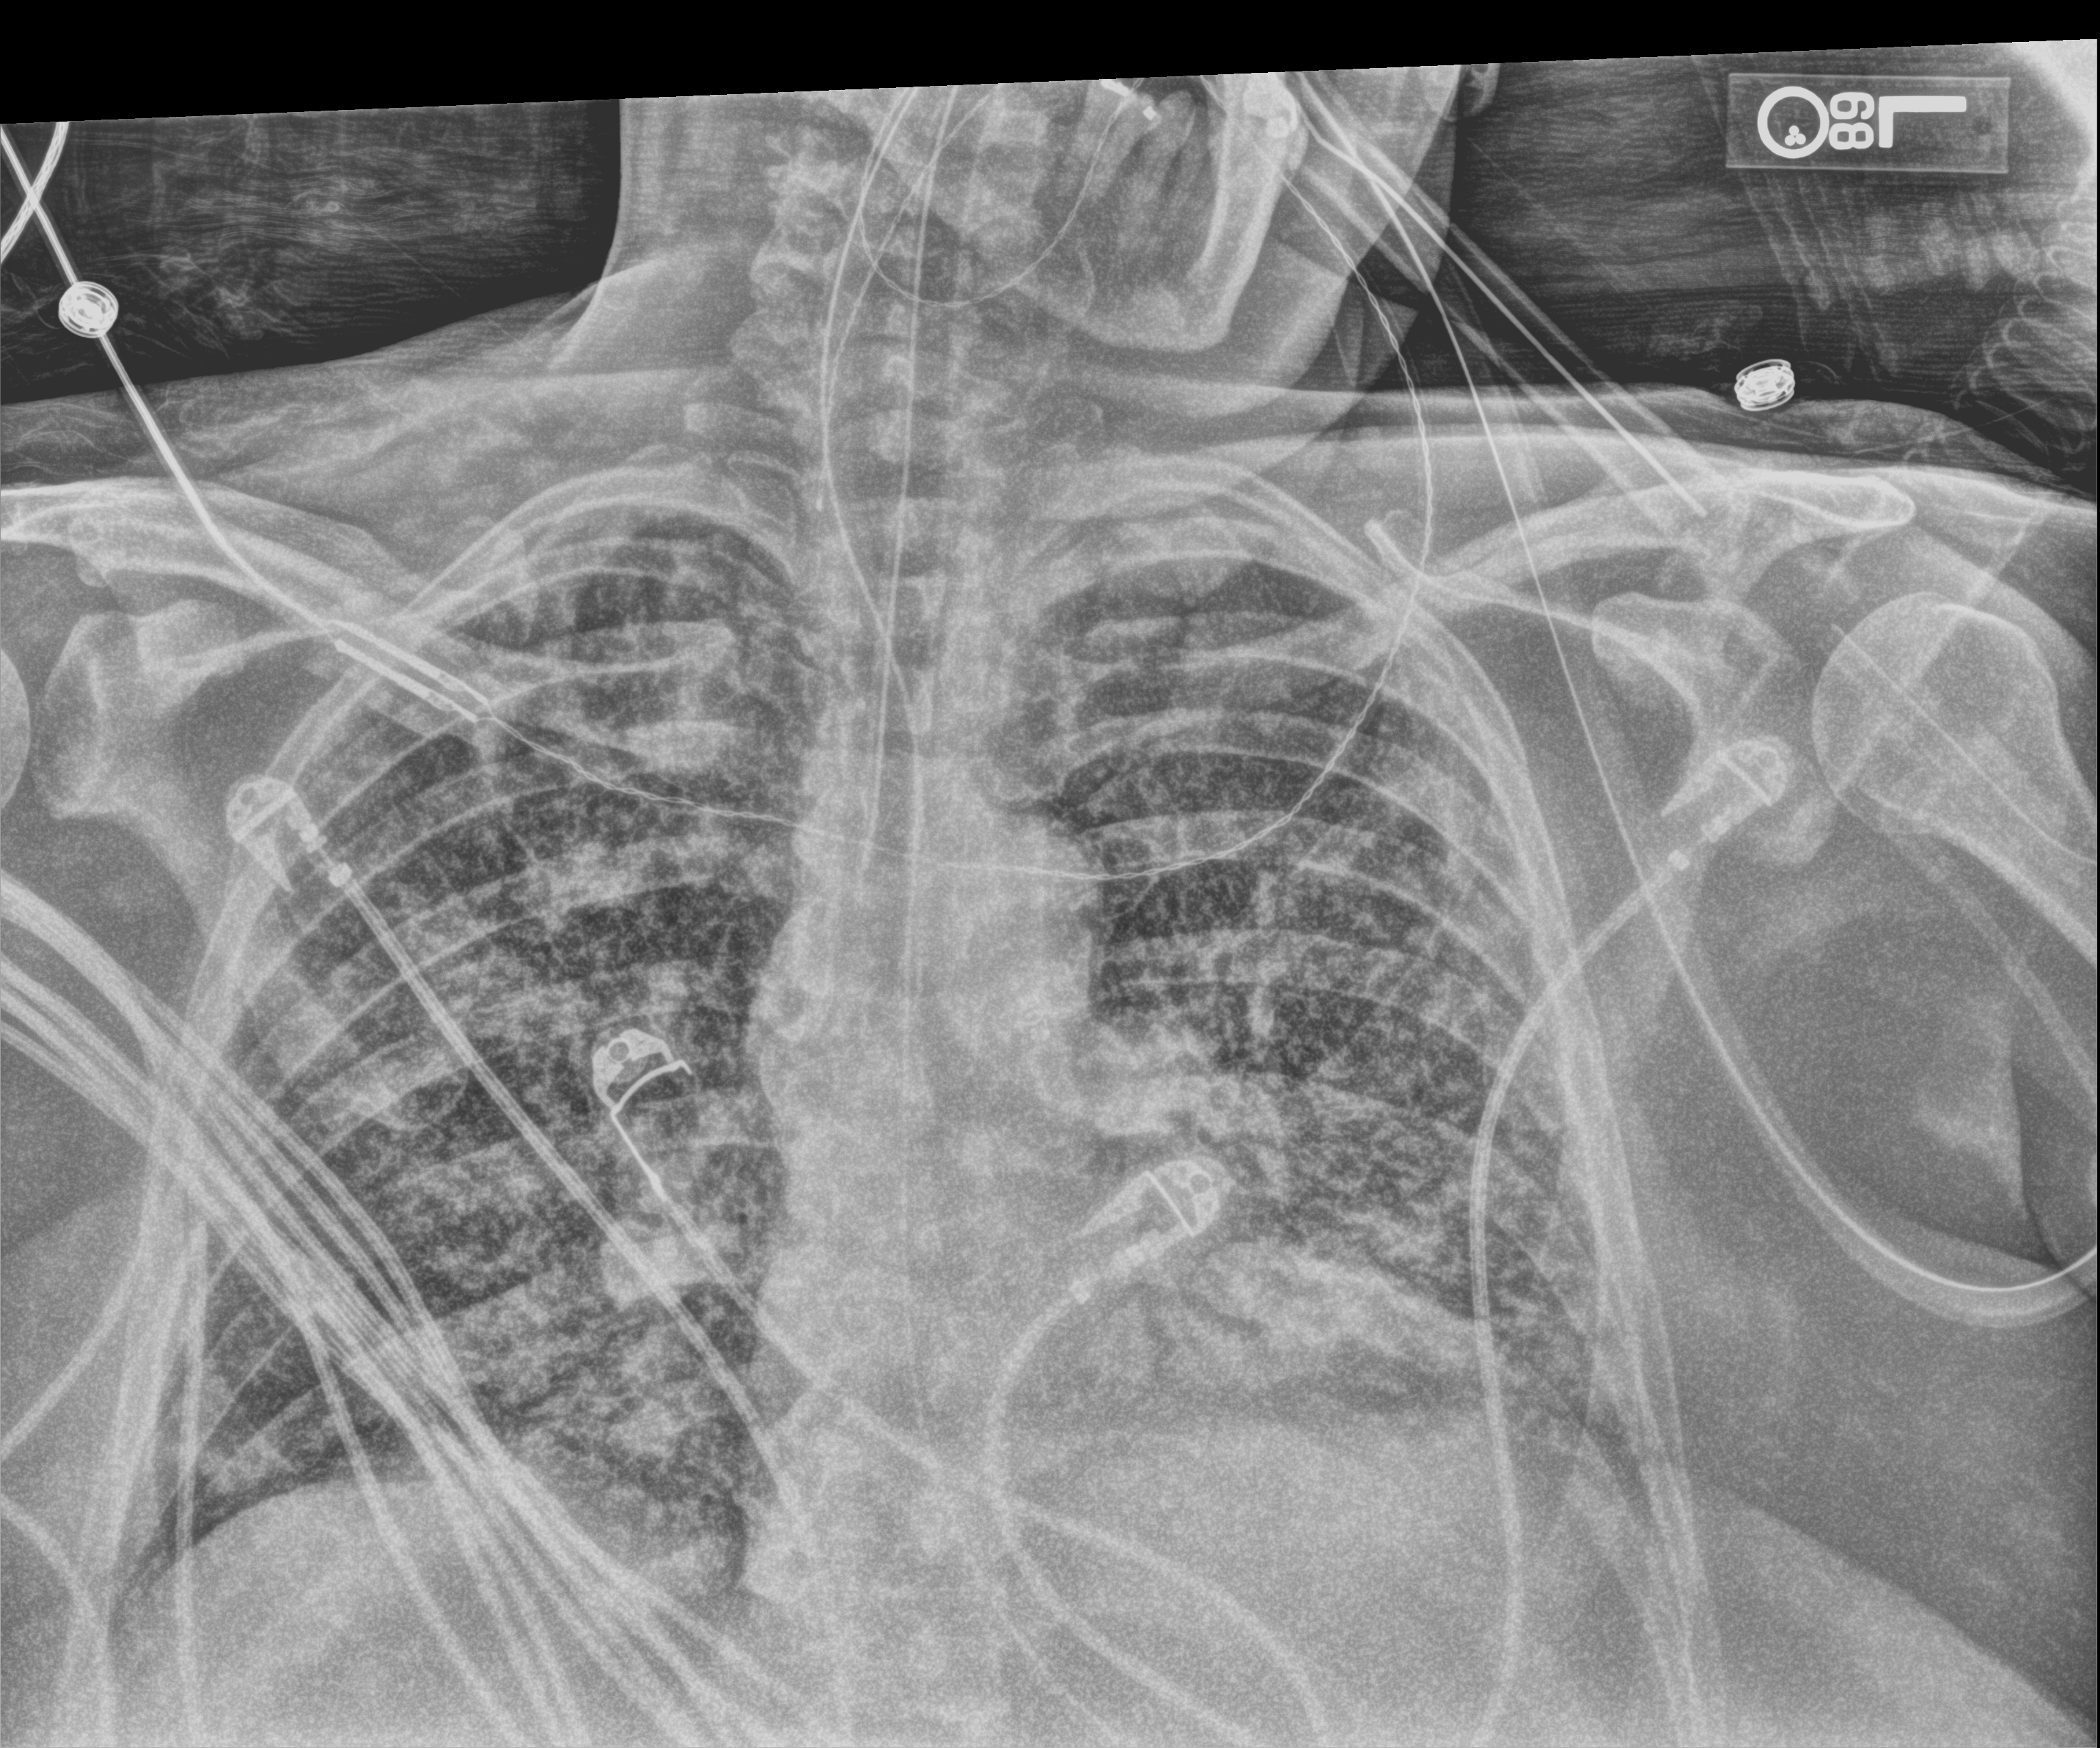
Chest X-ray (portable); anteroposterior (AP) projection. Patient hospitalised with COVID-19, aged 18–59 years.
Admission-level facts for this patient (not findings on this image; timing relative to this image not recorded): mechanically ventilated during this hospital stay: yes.